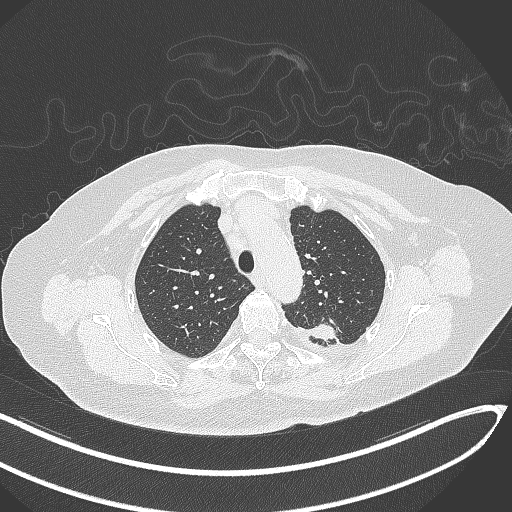
Chest CT, one axial slice; position 247 of 270 along the scan axis; reconstruction kernel B70f; 120 kVp; lung window (W 1500 / L -600 HU); 1 mm slice thickness; 512 × 512 image matrix, field of view 400 × 400 mm. Patient: female, 76 years. Case-level facts recorded for this patient, not image findings: clinical TNM (as recorded): T1c N0 M0.
Outlined on this slice (bounding box drawn by a radiologist):
- lung tumour (recorded histology: adenocarcinoma): box from (x=294, y=316) to (x=343, y=342) px